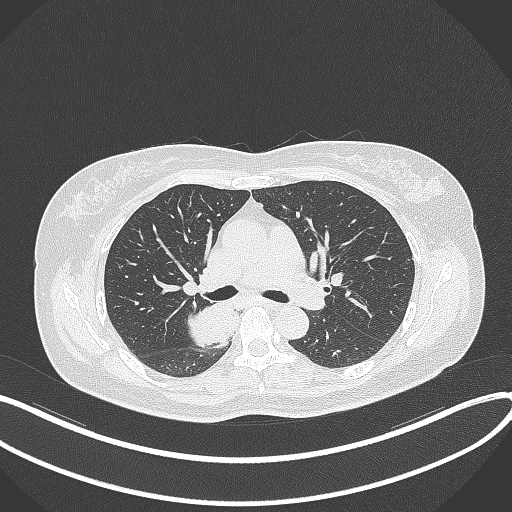
Chest CT, one axial slice; slice 226 of 331 in the series (ordered by position); reconstruction kernel B70f; 120 kVp; lung window (W 1500 / L -600 HU); 1 mm slice thickness; 512 × 512 image matrix, field of view 400 × 400 mm. Female patient, age 54 years. Case-level facts recorded for this patient, not image findings: clinical TNM (as recorded): T4 N0 M0.
Outlined on this slice (bounding box drawn by a radiologist):
- lung tumour (recorded histology: adenocarcinoma): bounding box <182,297,247,353> (left, top, right, bottom; pixels)